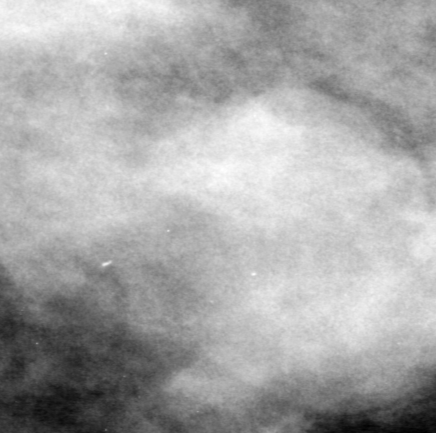
Region of interest cut from a scanned film mammogram (one marked finding), left breast, MLO view, BI-RADS breast density category 3 (scale 1–4).
Mass, shape lobulated, margins obscured; BI-RADS assessment category 0 (incomplete: needs additional imaging); subtlety rating 5 on a 1 (subtle) to 5 (obvious) scale; pathology result (as recorded, not read from the image): benign.